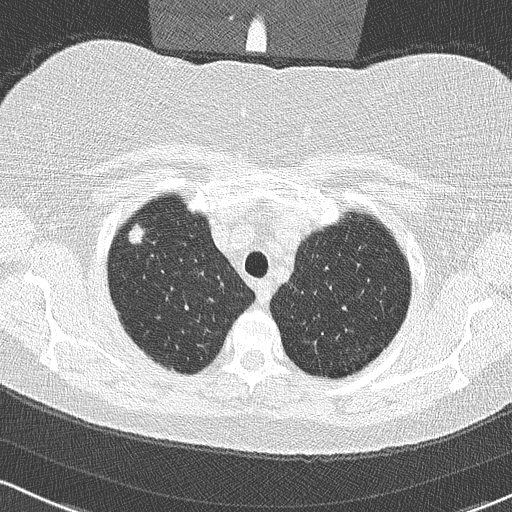
Low-dose screening chest CT, axial slice, third screening round (two years after baseline), lung window (W 1500 / L -600 HU), lung (sharp) reconstruction kernel (B50f), 120 kVp, slice 46 of 315 in the series. Female participant, aged 58 years at enrolment.
Expert-annotated lung lesion, bounding box (x1, y1, x2, y2) in pixels: (119, 218, 159, 256). The screening reader recorded 2 non-calcified nodules or masses ≥4 mm on this exam; which of them this box marks is not recorded. Official screen result: positive, other.